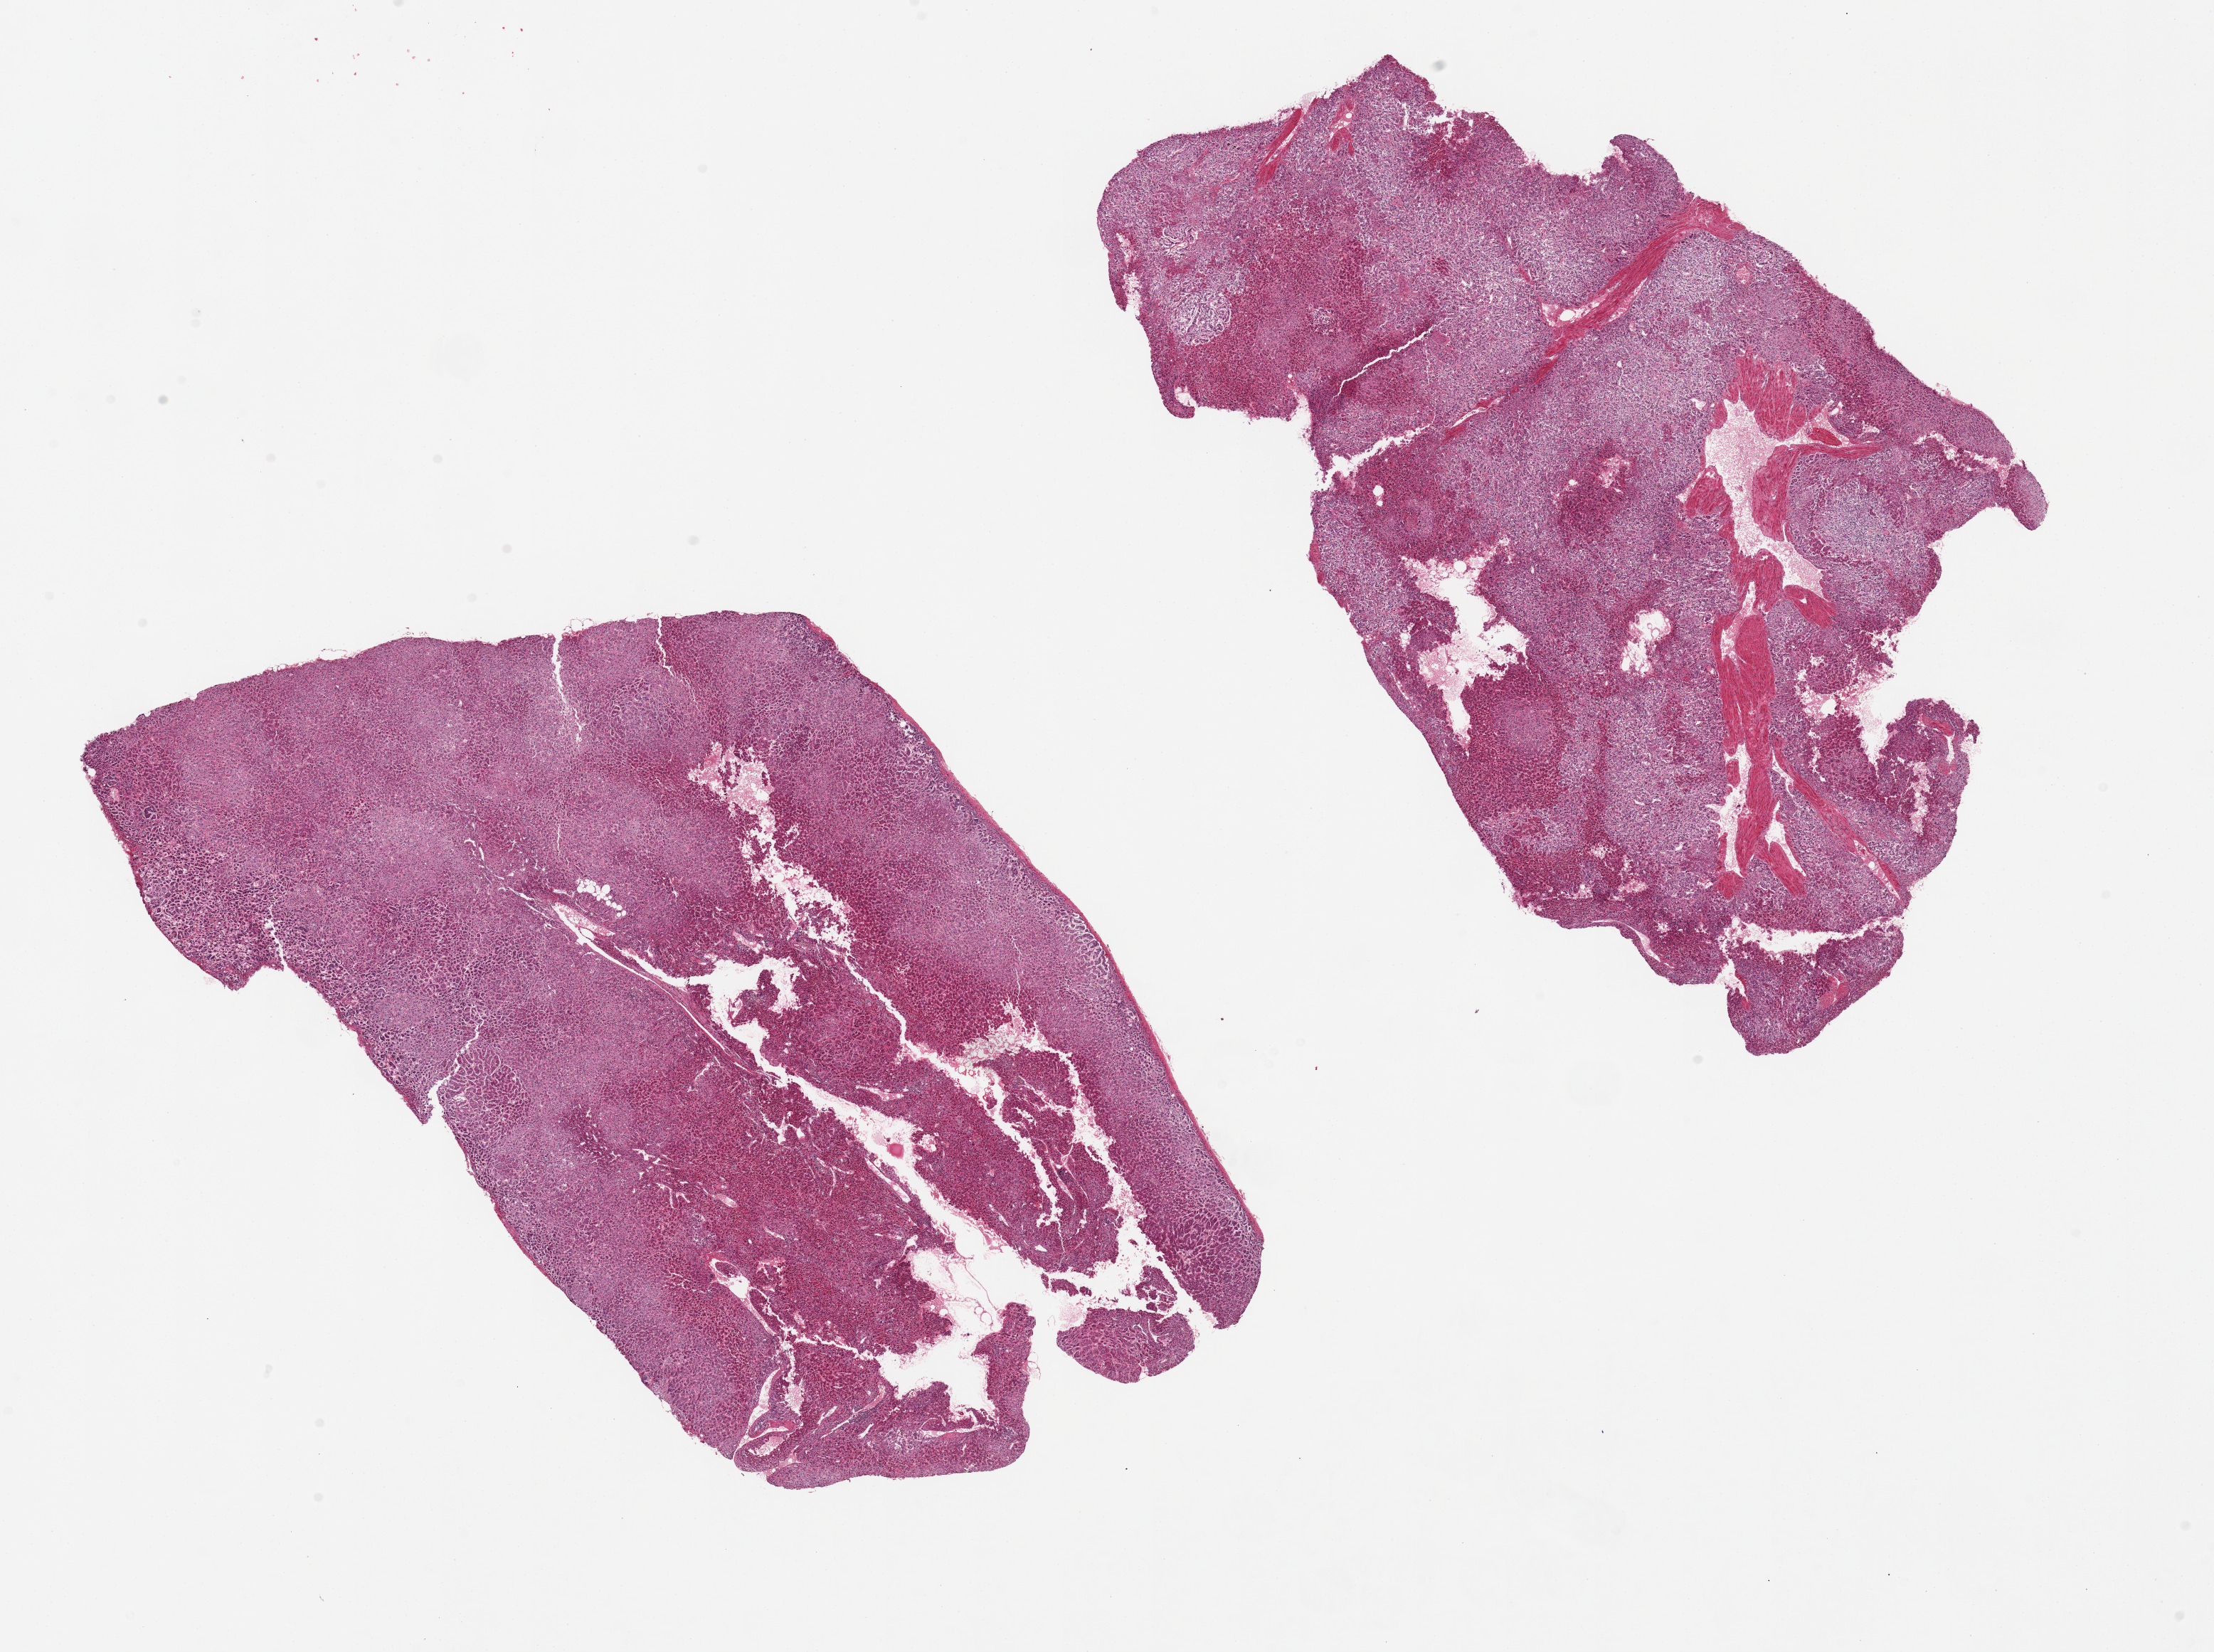
Whole-slide image, haematoxylin and eosin stain — low-resolution overview of the scanned area, about 24.6 x 18.4 mm; PAXgene-fixed, paraffin-embedded tissue; sampled site (target tissue): adrenal gland; donor tissue sample. Donor: female.
Pathologist's review note for this sample: 2 pieces, 12x8 & 12x8mm; all cortex, moderate-severe autolysis.